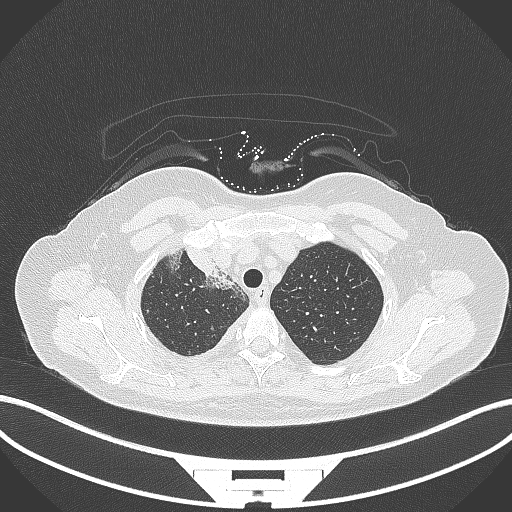
Chest CT, one axial slice. Slice 257 of 305 in the series (ordered by position). Reconstruction kernel B70f. Lung window (W 1500 / L -600 HU). 512 × 512 image matrix. Female patient, age 52 years. Case-level facts recorded for this patient, not image findings: clinical TNM (as recorded): T3 N1 M1.
Outlined on this slice (rectangle marked by the reading radiologist):
- lung tumour (recorded histology: adenocarcinoma): bounding box (x1, y1, x2, y2) in pixels: (183, 240, 219, 280)